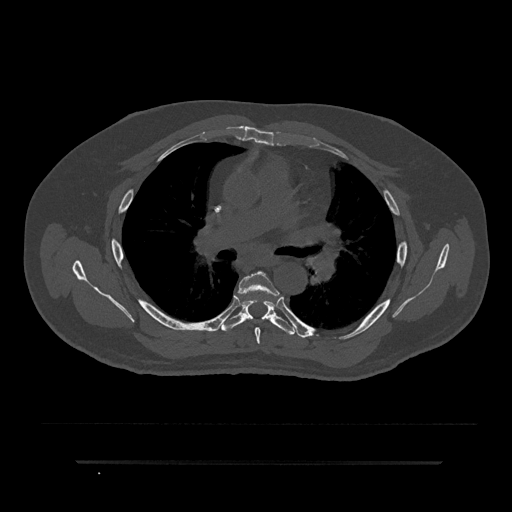
CT including the spine, one axial slice; slice 549 of 797 in the series (ordered by position); bone window (W 1800 / L 400 HU); 0.5 mm slice thickness; 512 × 512 image matrix, field of view 464 × 464 mm. Male patient, age 59 years. From the clinical record (not read from this slice): primary cancer: bile ducts.
Structures marked on this image (semi-automatic segmentation, software-assisted and operator-edited):
- T5 vertebra: bounding box (x1, y1, x2, y2) in pixels: (239, 271, 277, 345)
- T6 vertebra: (221, 301, 294, 335)